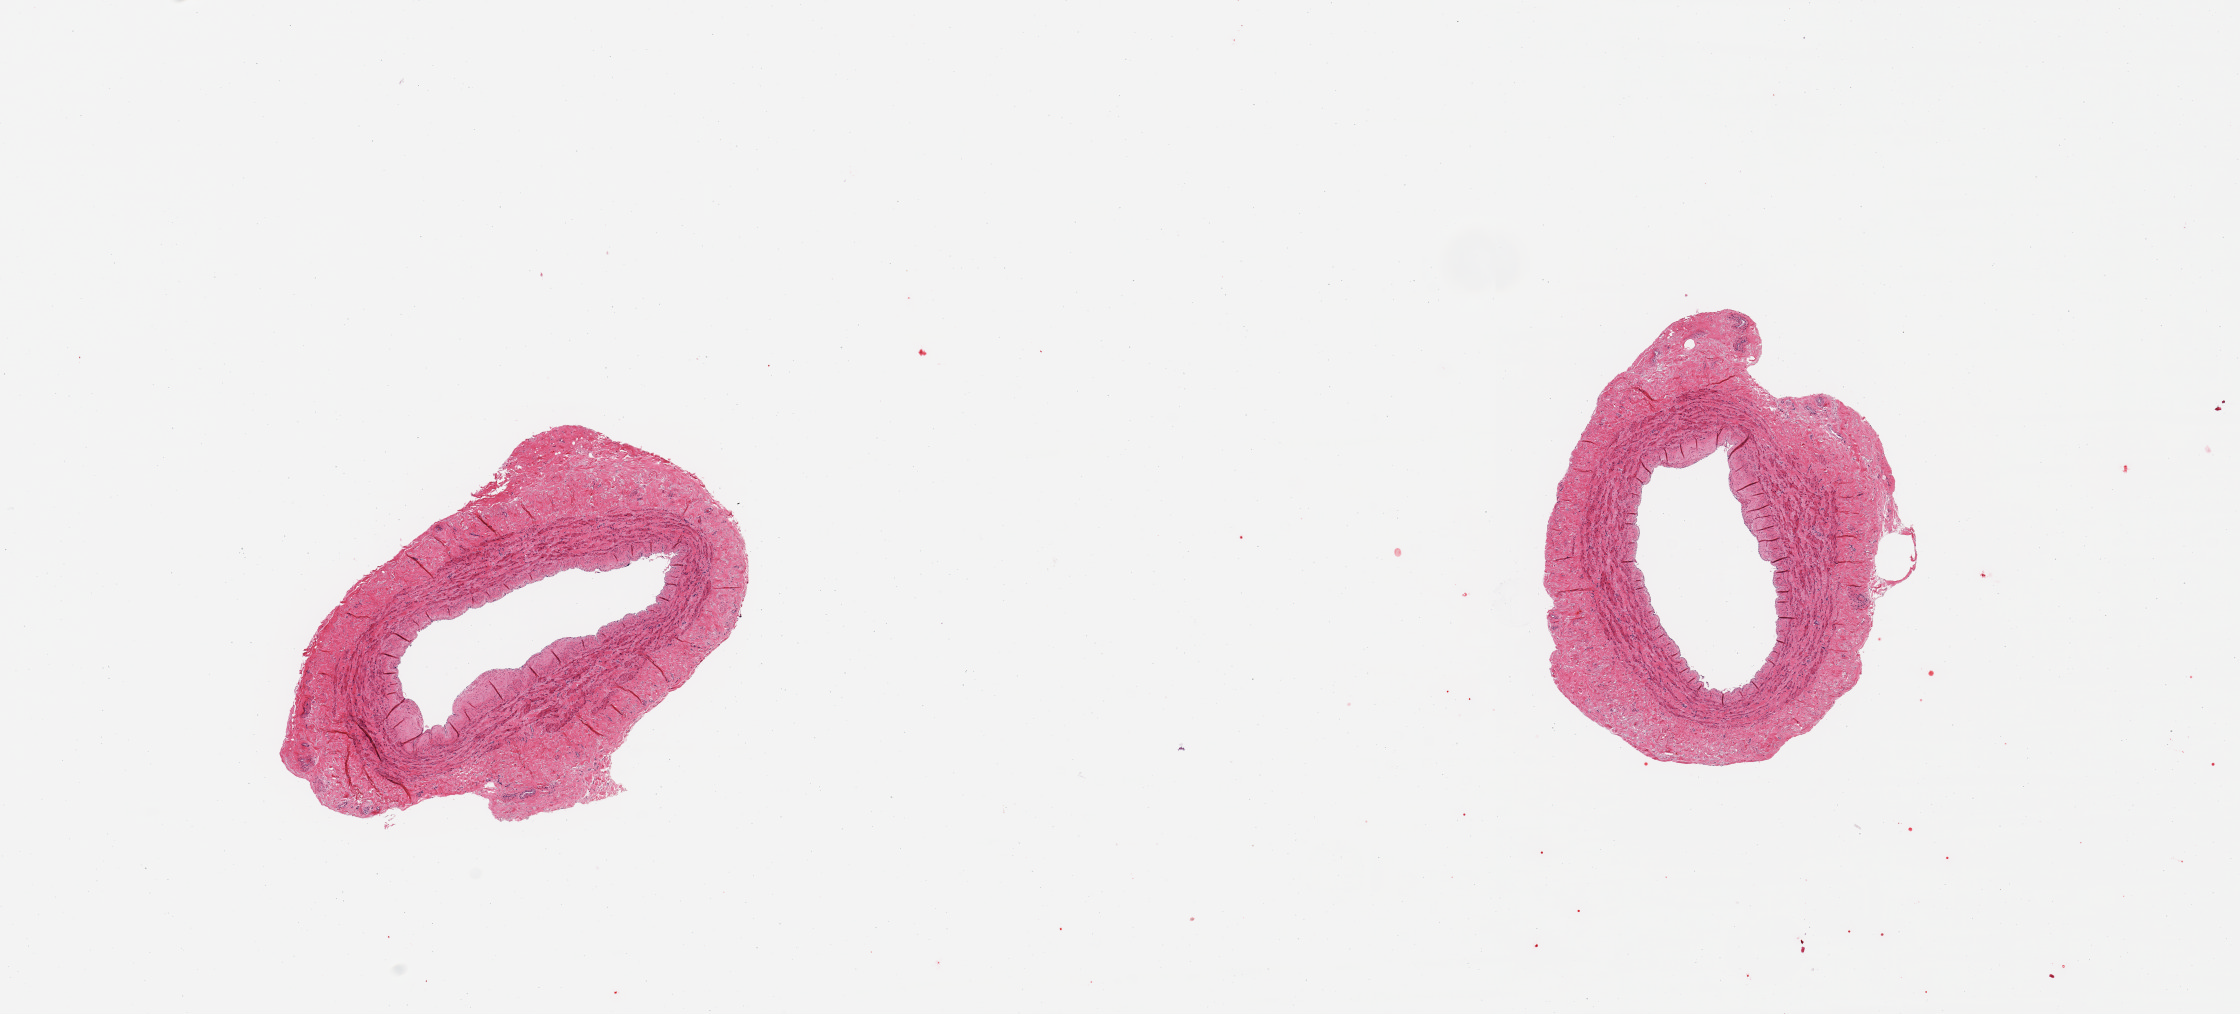
Haematoxylin and eosin whole-slide image, a low-resolution overview of the entire scanned area, about 17.7 x 8.0 mm (slide scanned at 20x), PAXgene-fixed paraffin-embedded (PFPE) section, section of tibial artery (target tissue), donor tissue sample. Donor sex: male.
Review note (as recorded): 2 pieces, confirmed artery, adherent rim of fibrous tissue up to ~0.4mm.